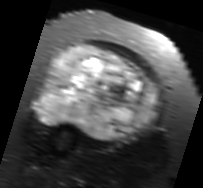
MRI of an extremity soft-tissue mass, one axial slice; position 42 of 91 along the scan axis; T2-weighted fat-saturated; MR volume resampled by the dataset authors to the PET/CT grid (not the native acquisition matrix); 3.27 mm slice thickness; 203 × 188 image matrix, field of view 198 × 184 mm. Female patient. From the clinical record (not read from this slice): histological type: malignant solitary fibrous tumor; grade: intermediate; site of the primary tumour: right thigh.
Annotated regions visible in this slice (expert contour drawn on MRI and transferred to this co-registered scan by the dataset authors):
- gross tumour volume including surrounding oedema: bounding box (x1, y1, x2, y2) in pixels: (31, 44, 162, 141)
- gross tumour volume (mass): (38, 44, 157, 139)